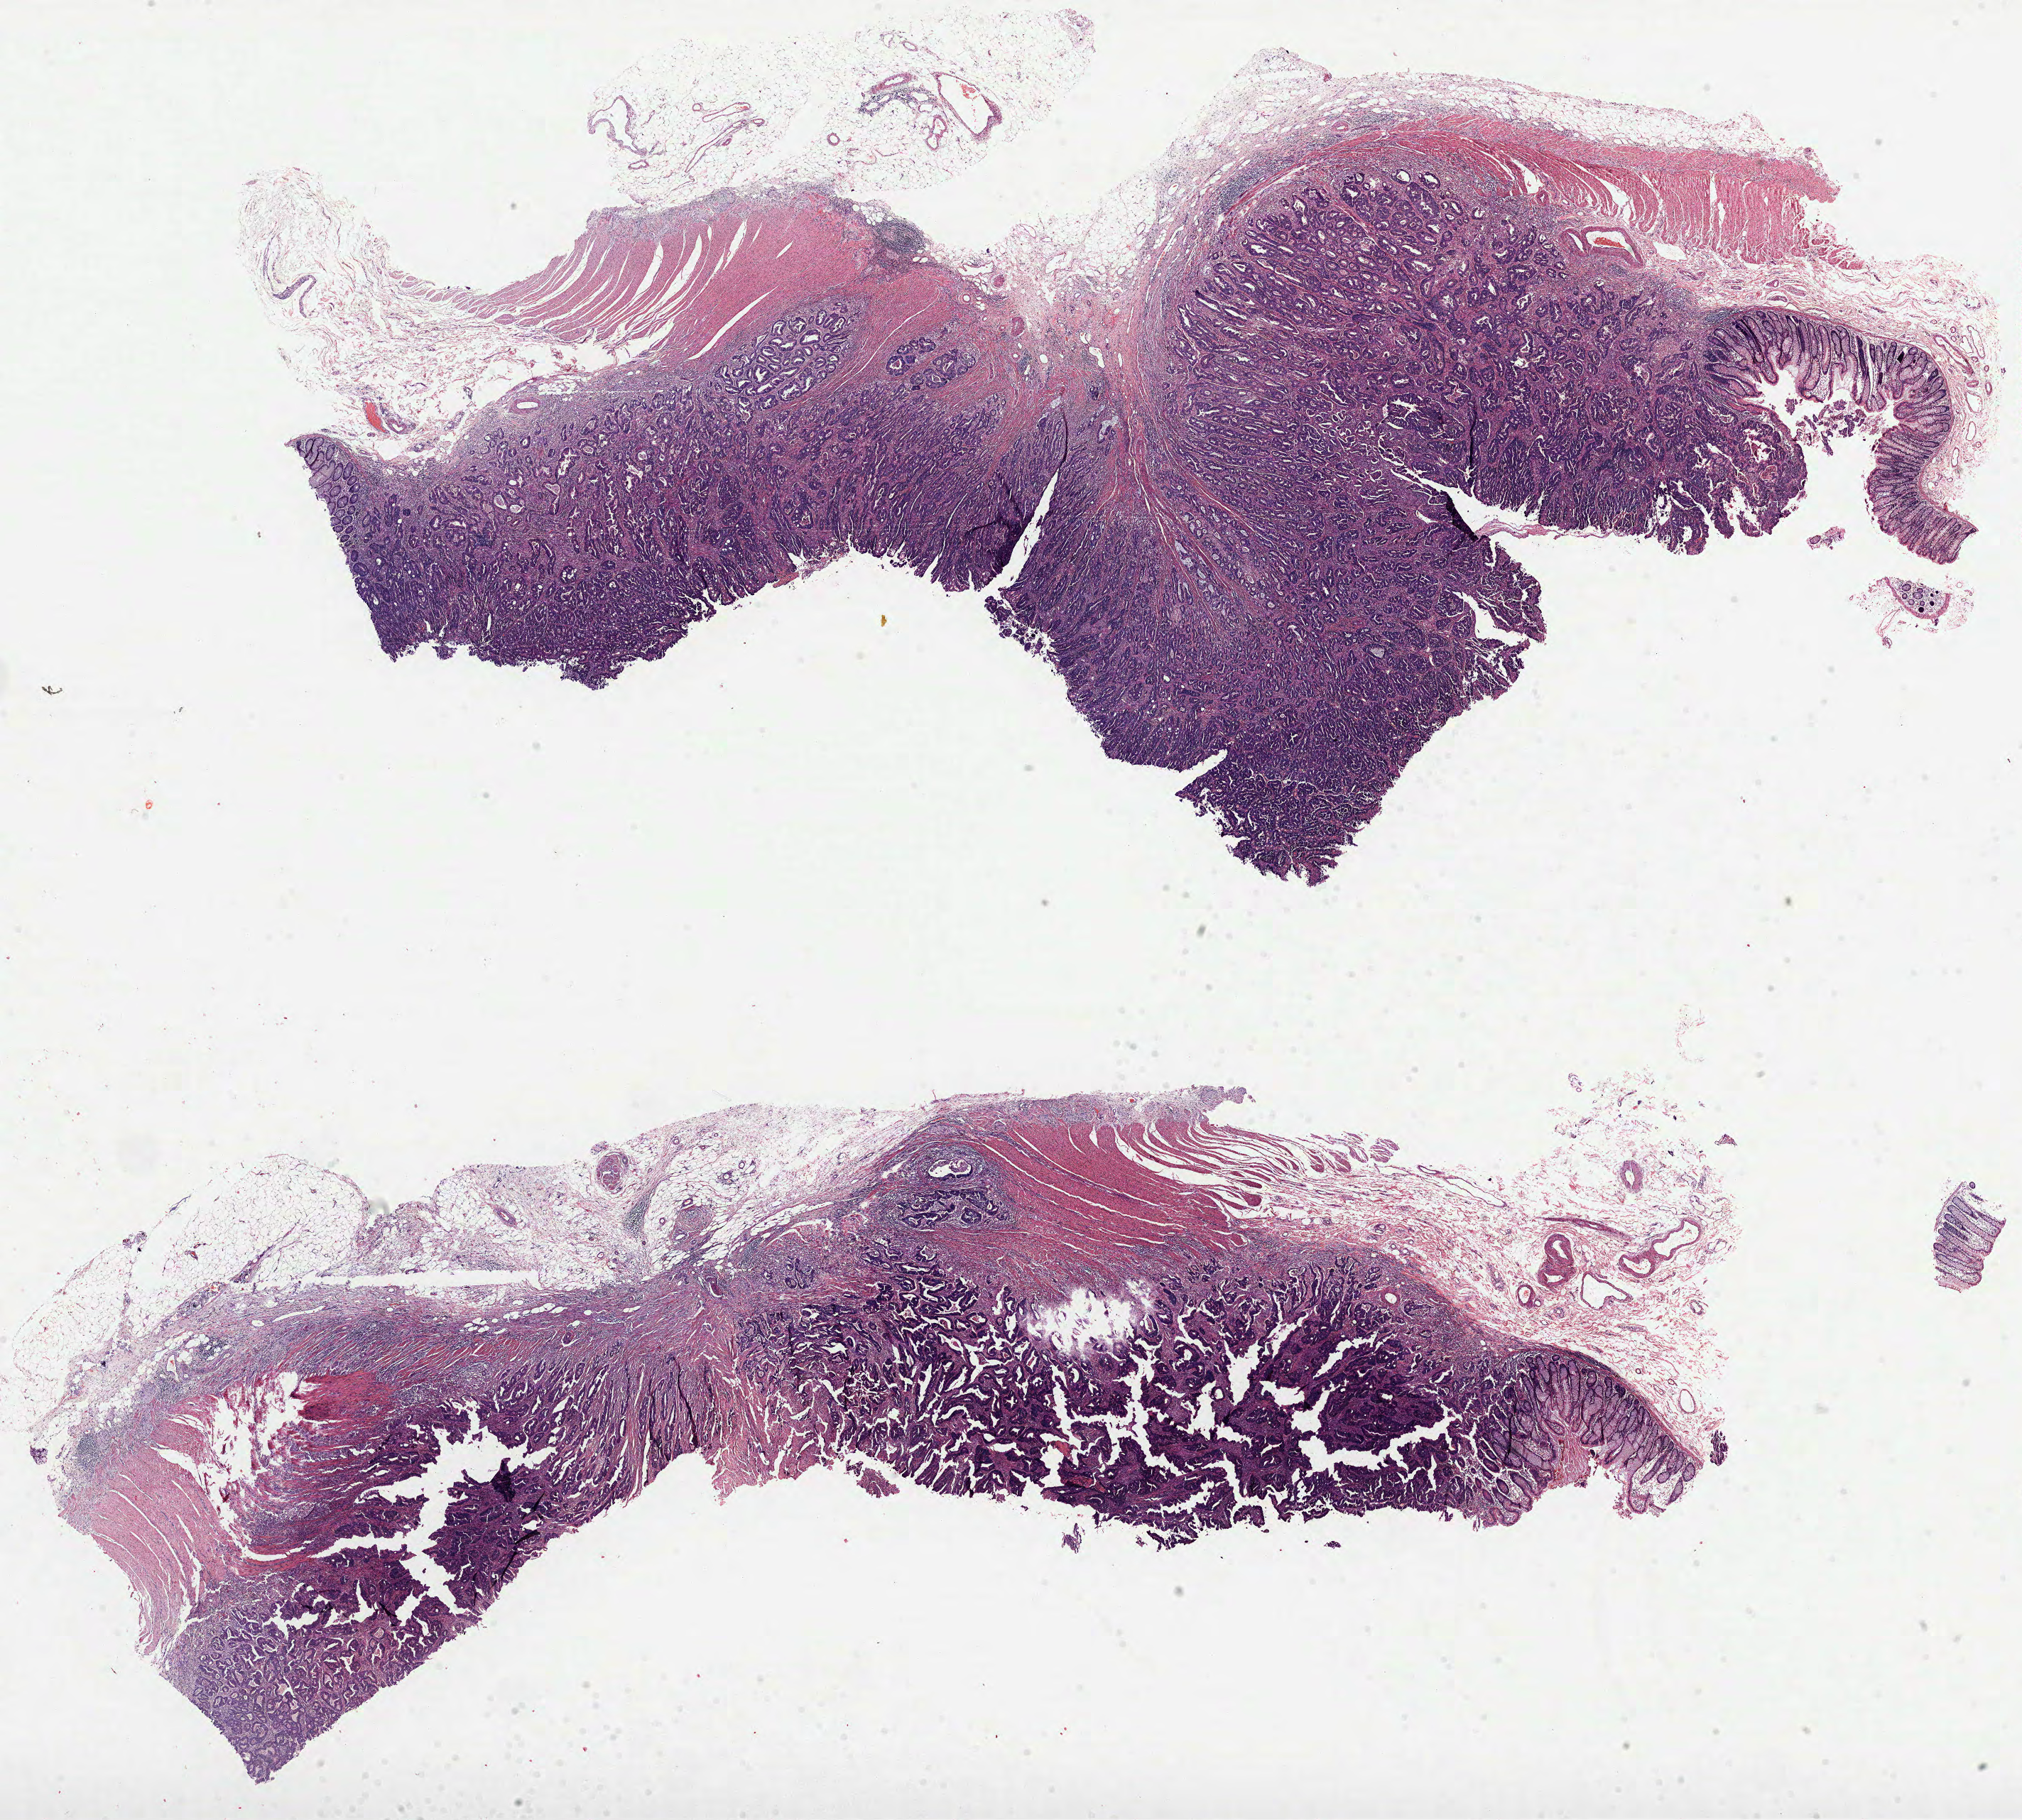
Whole-slide histology image, H&E-stained — low-resolution overview of the scanned area, about 23.0 x 20.7 mm (acquisition: 40x scan); FFPE section; colon, primary tumour sample. Female, age 79 years at initial diagnosis.
Histologic diagnosis: Adenocarcinoma, NOS (ascending colon).